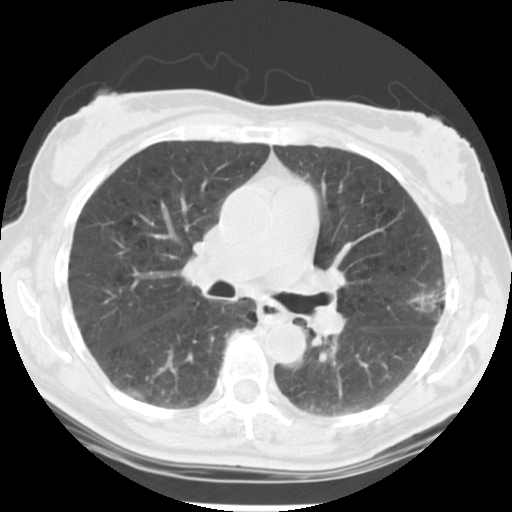
Low-dose screening chest CT, one axial slice. Slice 128 of 223 in the series (ordered by position). Reconstruction kernel STANDARD. 120 kVp. Lung window (W 1500 / L -600 HU). 512 × 512 image matrix, field of view 302 × 302 mm.
Structures marked on this image (outlined manually by an expert reader):
- lesion 1 (tumor, upper lobe of left lung): box from (x=408, y=286) to (x=445, y=321) px